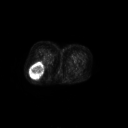
FDG PET of an extremity soft-tissue mass (from a PET/CT study), one axial slice. Slice 37 of 267 in the series (ordered by position). 128 × 128 image matrix, field of view 700 × 700 mm. Female patient, age 70 years. From the clinical record (not read from this slice): histological type: synovial sarcoma; grade: intermediate; site of the primary tumour: right buttock.
Annotated regions visible in this slice (expert contour drawn on MRI and transferred to this co-registered scan by the dataset authors):
- gross tumour volume including surrounding oedema: box from (x=29, y=60) to (x=44, y=78) px
- gross tumour volume (mass): (x=29, y=62)–(x=44, y=78)